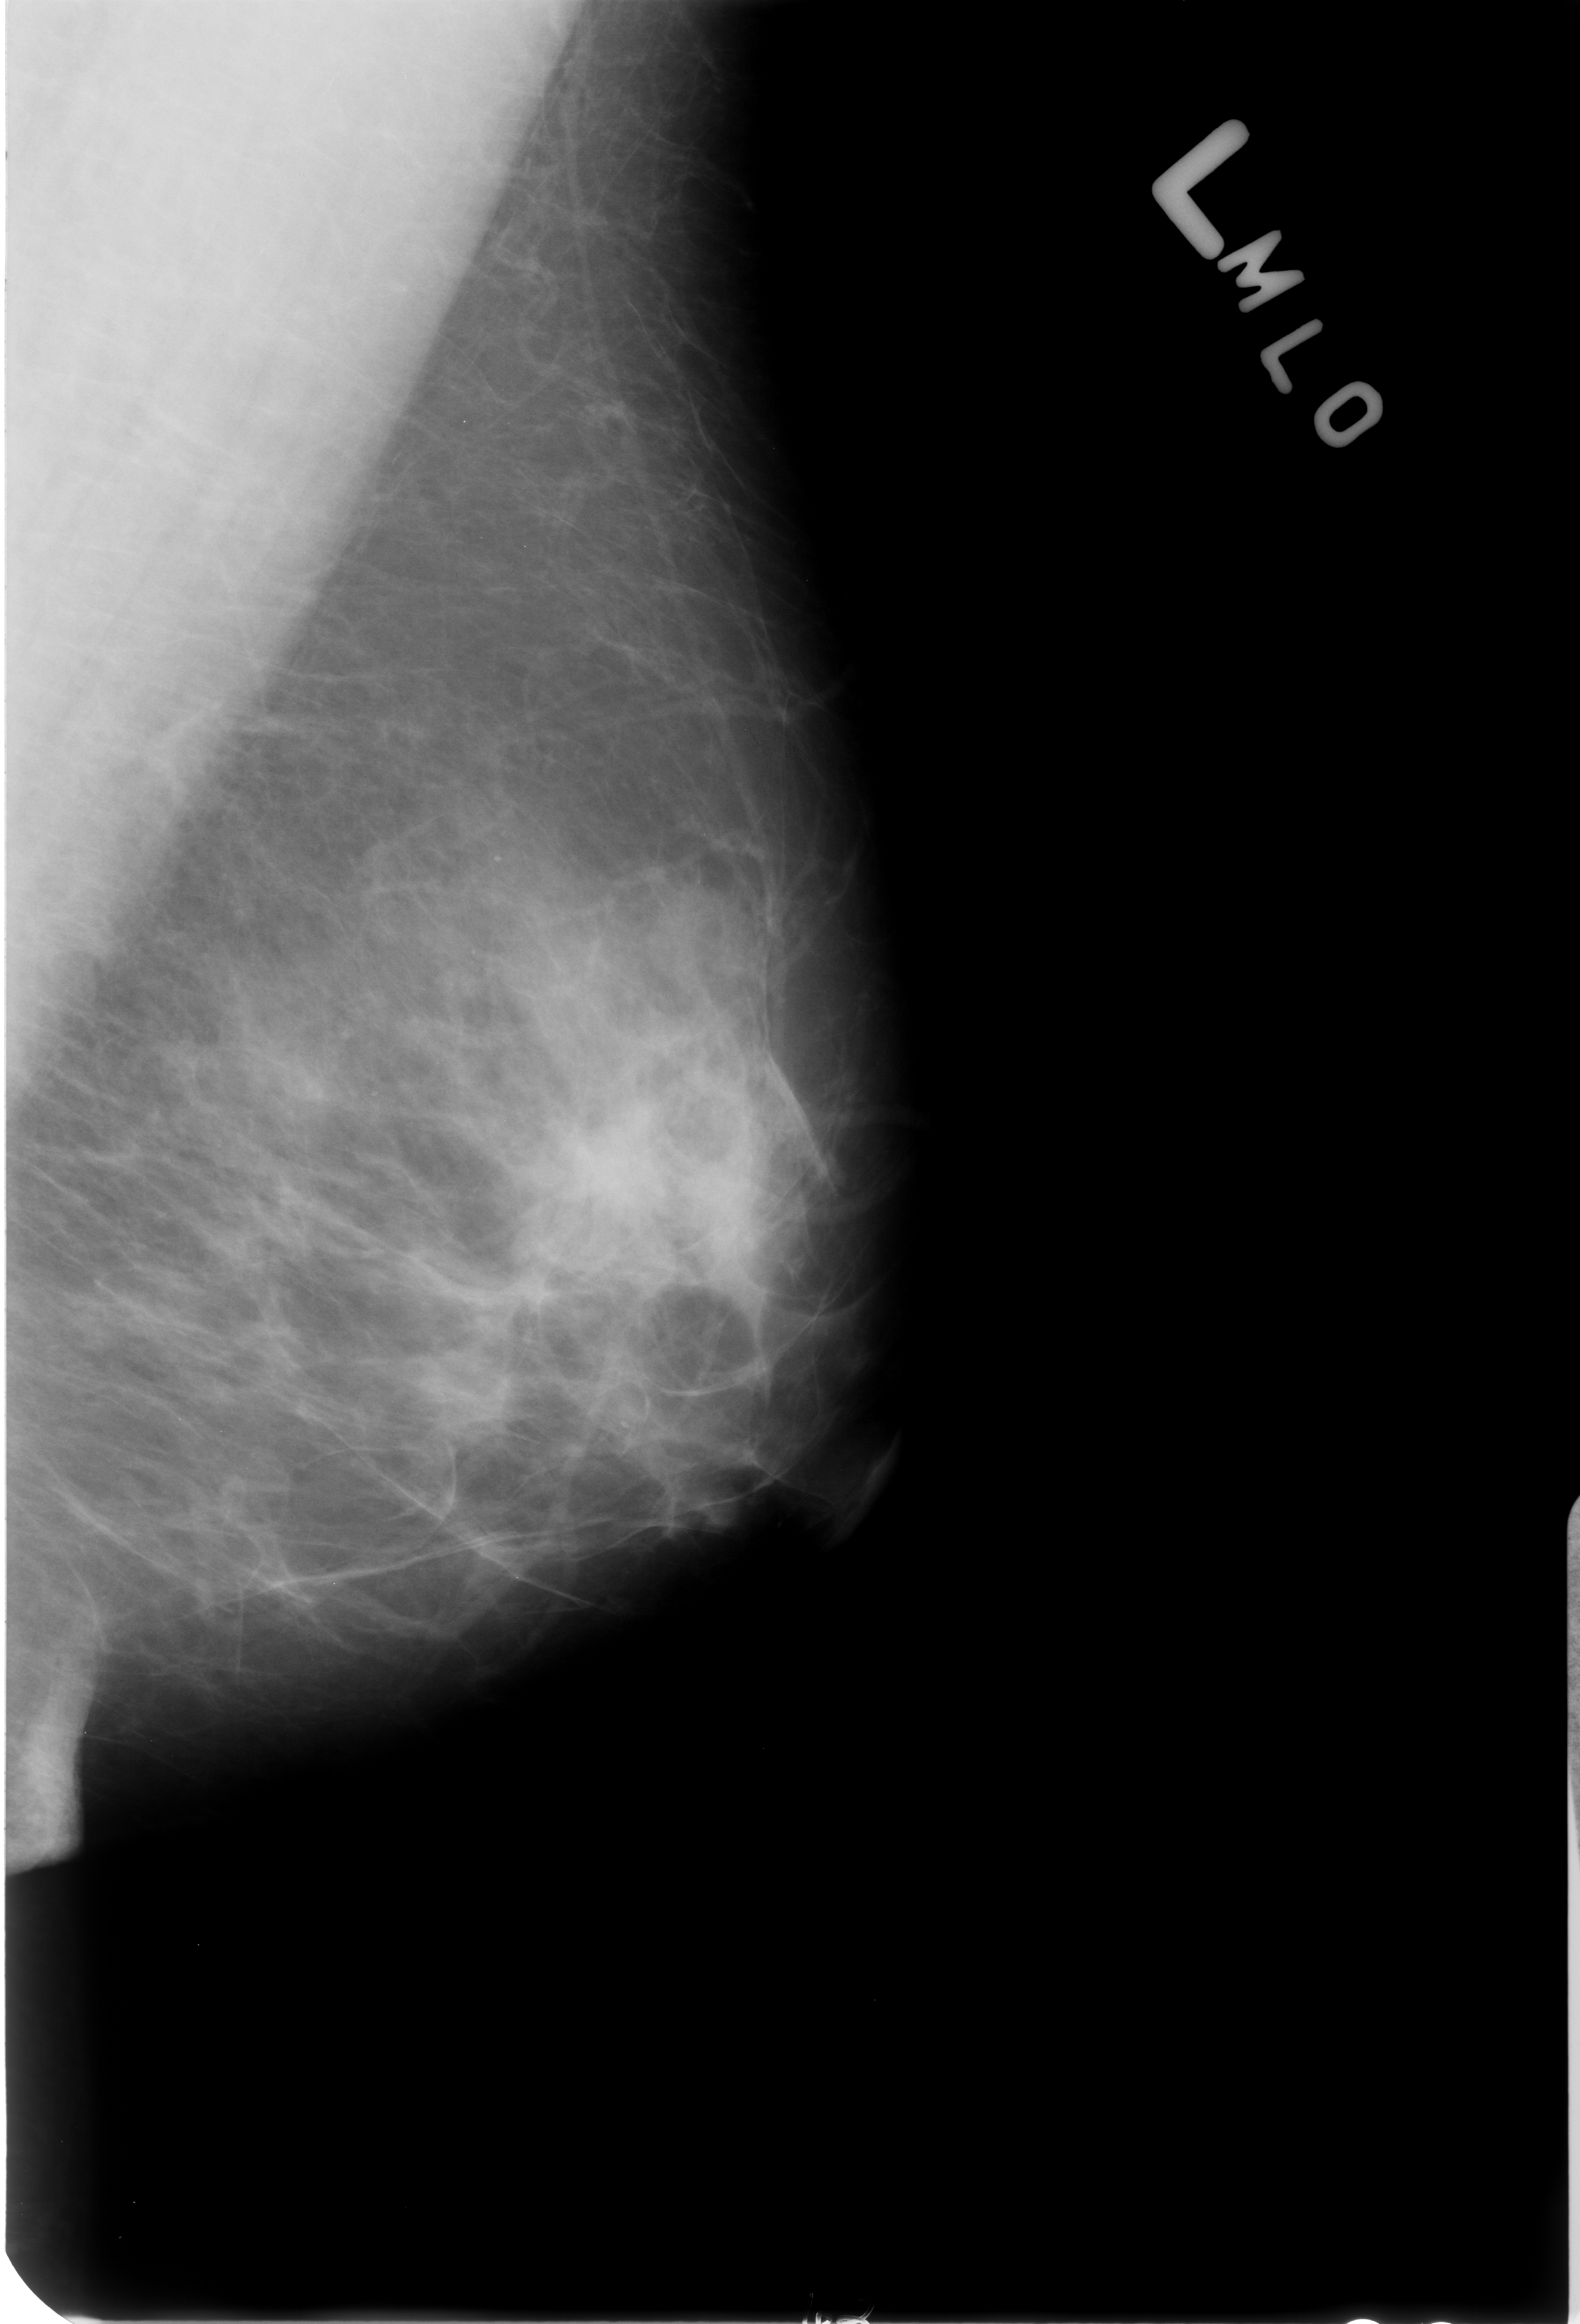
Digitized screen-film mammogram; left breast; MLO view; breast composition: heterogeneously dense (BI-RADS density category 3 of 4).
Radiologist-marked abnormalities on this image: calcifications, morphology punctate, distribution segmental; BI-RADS assessment category 2; subtlety rating 3 on a 1 (subtle) to 5 (obvious) scale; benign; no additional work-up was recommended (benign without callback).